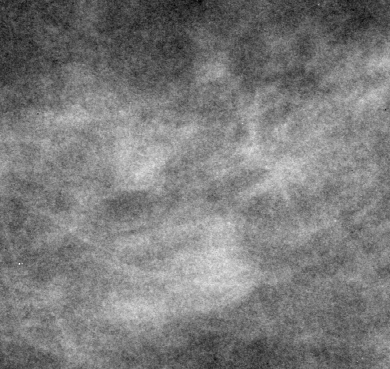
Region of interest cut from a scanned film mammogram (one marked finding); left breast; CC view.
Marked abnormality: mass, shape irregular, margins spiculated; BI-RADS assessment category 5; subtlety rating 5 on a 1 (subtle) to 5 (obvious) scale; pathology result (as recorded, not read from the image): malignant.